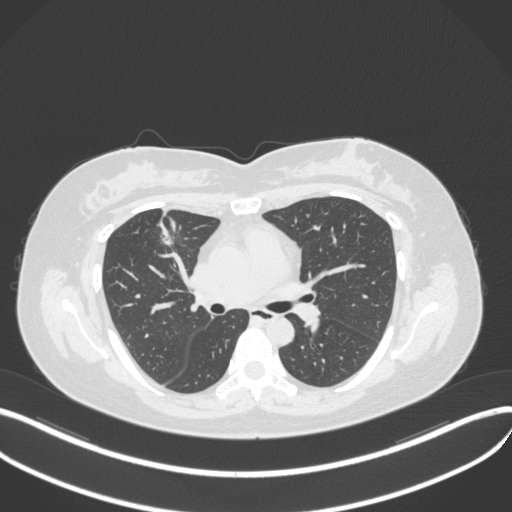
Chest CT, one axial slice; reconstruction kernel B31f; lung window (W 1500 / L -600 HU); 1 mm slice thickness; 512 × 512 image matrix, field of view 400 × 400 mm. Female patient, age 42 years. Case-level facts recorded for this patient, not image findings: clinical TNM (as recorded): T1b N0 M0.
Structures marked on this image (rectangle marked by the reading radiologist):
- lung tumour (recorded histology: adenocarcinoma): bounding box <160,225,176,245> (left, top, right, bottom; pixels)